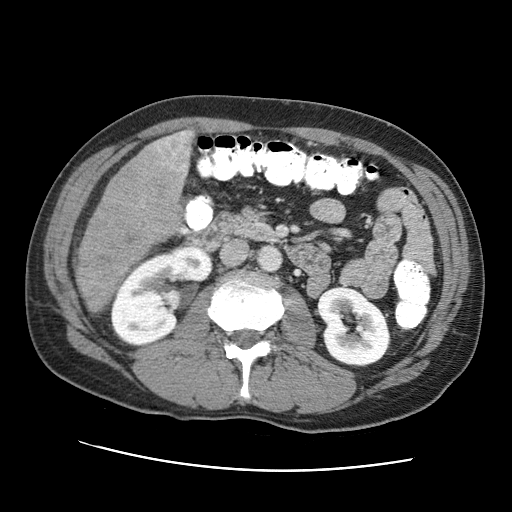
Contrast-enhanced abdominal CT (liver protocol), one axial slice; slice 21 of 95 in the series (ordered by position); reconstruction kernel STANDARD; 120 kVp; one of 2 acquisitions stored at this slice position; soft-tissue window (W 400 / L 40 HU); 512 × 512 image matrix. Case-level facts recorded for this patient, not image findings: diagnosis: hepatocellular carcinoma (patient treated with transarterial chemoembolisation; whether this scan precedes or follows treatment is not stated here); TNM stage (as recorded): Stage-IVA; Child-Pugh class: A; tumour differentiation: moderately differentiated; tumour nodularity: multinodular.
Outlined on this slice (semi-automatic segmentation, software-assisted and operator-edited):
- liver parenchyma outside the tumour (the mass and vessels are separate outlines, so this box may not span the whole liver): box from (x=110, y=130) to (x=194, y=298) px
- mass: (x=74, y=130)–(x=189, y=314)
- liver vessels: (x=189, y=132)–(x=192, y=135)